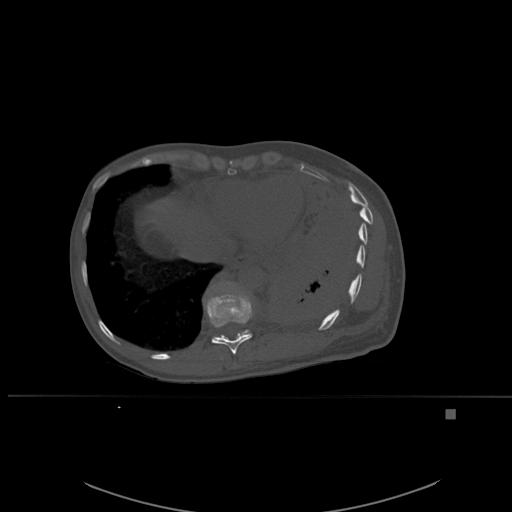
CT including the spine, one axial slice; position 314 of 537 along the scan axis; bone window (W 1800 / L 400 HU); 512 × 512 image matrix, field of view 440 × 440 mm. Female patient, age 45 years. Case-level facts recorded for this patient, not image findings: primary cancer: lung.
Structures marked on this image (semi-automatically segmented with operator editing):
- T10 vertebra: bounding box [x1, y1, x2, y2] px = [204, 286, 253, 355]
- T11 vertebra: [214, 281, 250, 340]